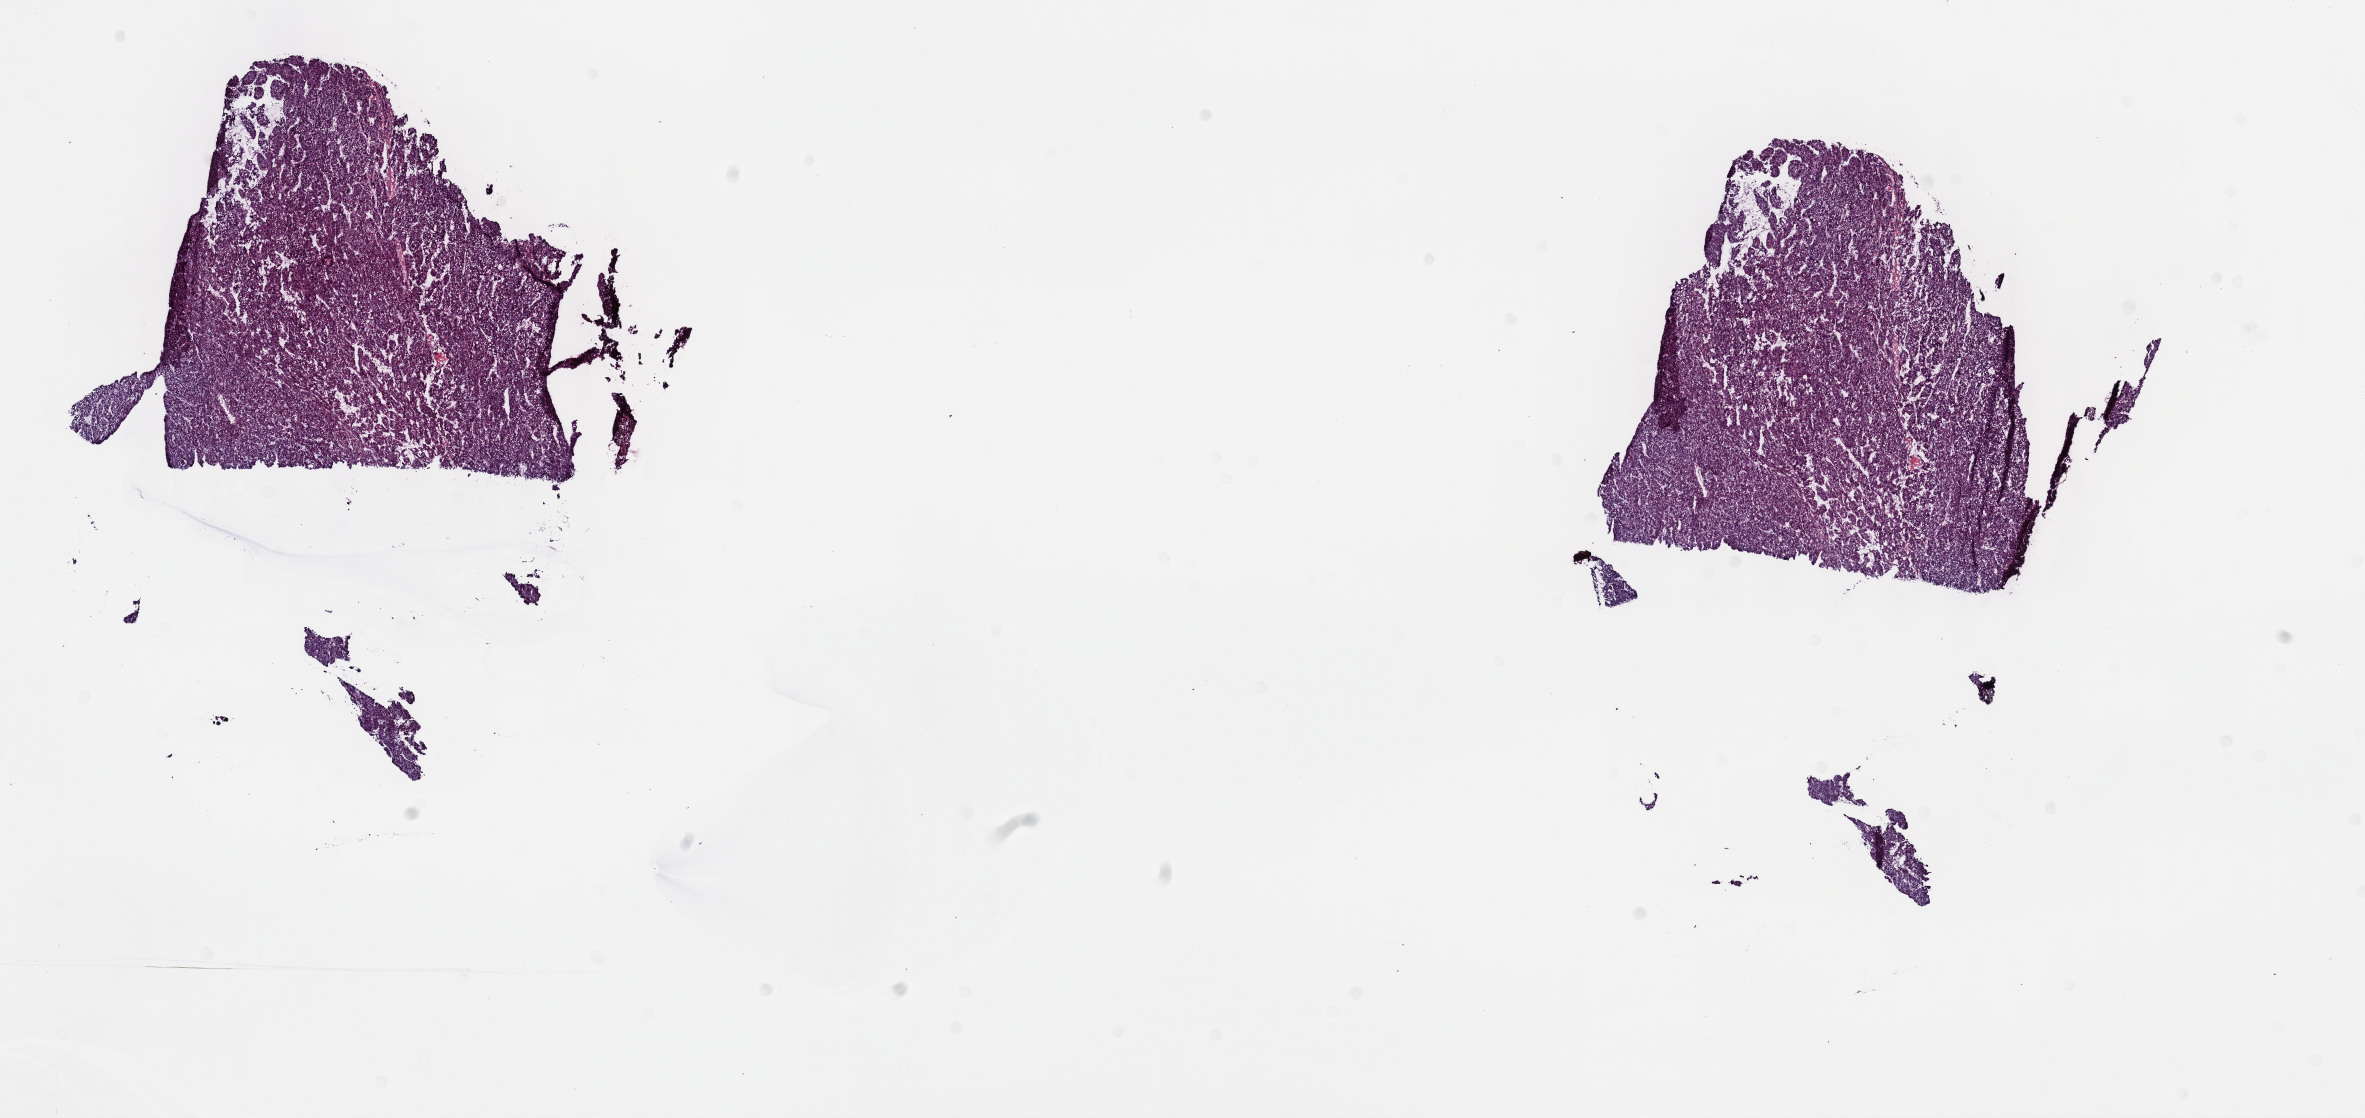
Digitized H&E tissue section (whole slide), a low-resolution overview of the entire scanned area, about 19.1 x 9.0 mm (from a 40x scan). Frozen section. Primary tumour sample from the liver. Male patient; age at initial diagnosis 75 years. Histologic grade: G2 (moderately differentiated). Slide review estimates, as recorded: tumour cells 80%, tumour nuclei 80%, normal cells 0%, stromal cells 20%, necrosis 0%. Infiltration values recorded for this section: lymphocyte infiltration 3%, monocyte infiltration 1%, neutrophil infiltration 2%.
AJCC pathologic stage: II (6th edition). Diagnosis: Hepatocellular carcinoma, NOS.